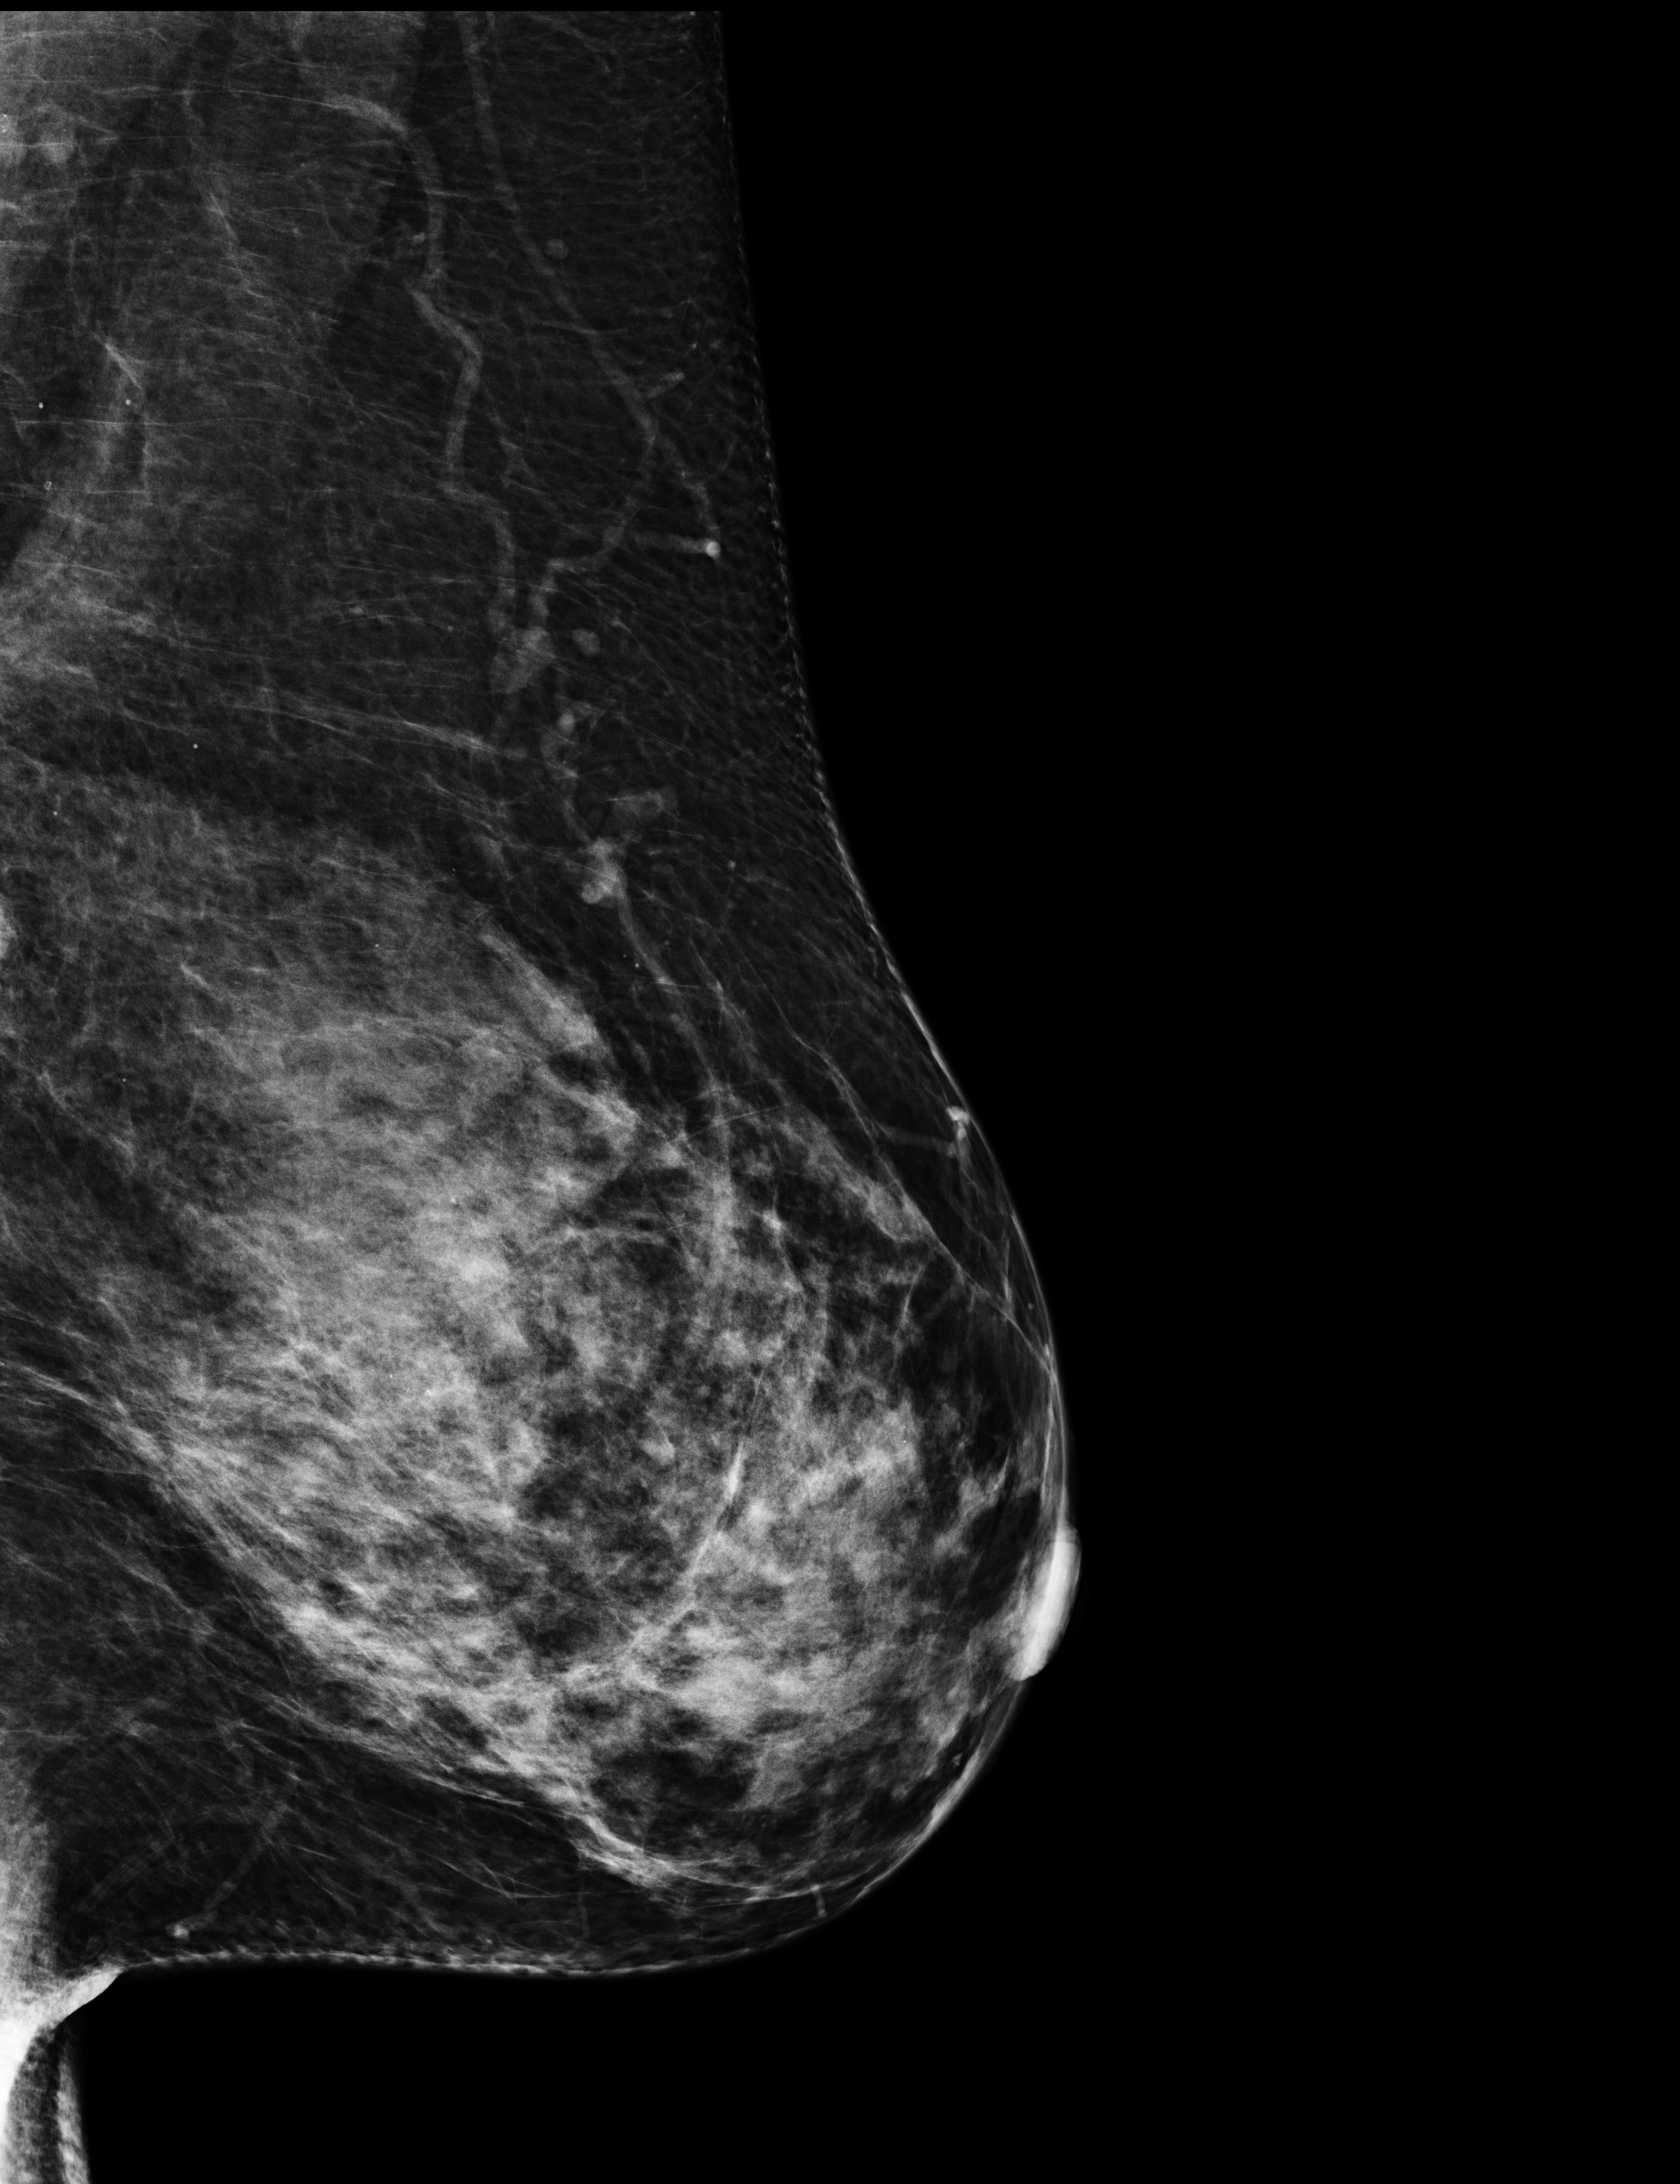
Screening examination, compressed breast thickness 76 mm. Female patient, age 47 years.
Image type: full-field digital mammogram. Breast: left. Projection: medio-lateral oblique projection.